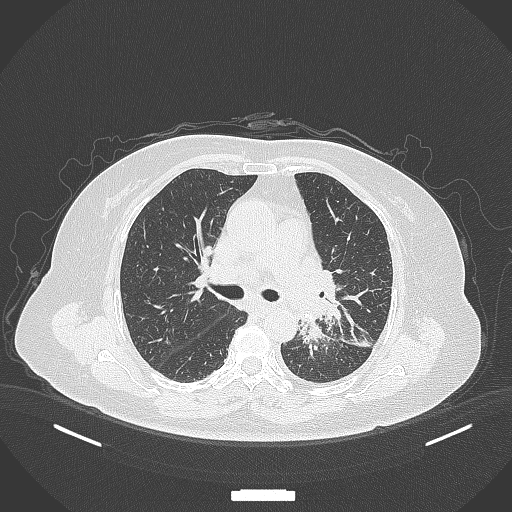
Chest CT, one axial slice. Slice 217 of 322 in the series (ordered by position). Reconstruction kernel B70f. 120 kVp. Lung window (W 1500 / L -600 HU). 1 mm slice thickness. 512 × 512 image matrix. Patient: female, 69 years. Case-level facts recorded for this patient, not image findings: clinical TNM (as recorded): T2b N3 M1.
Annotated regions visible in this slice (bounding box drawn by a radiologist):
- lung tumour (recorded histology: adenocarcinoma): bounding box (x1, y1, x2, y2) in pixels: (298, 314, 327, 351)